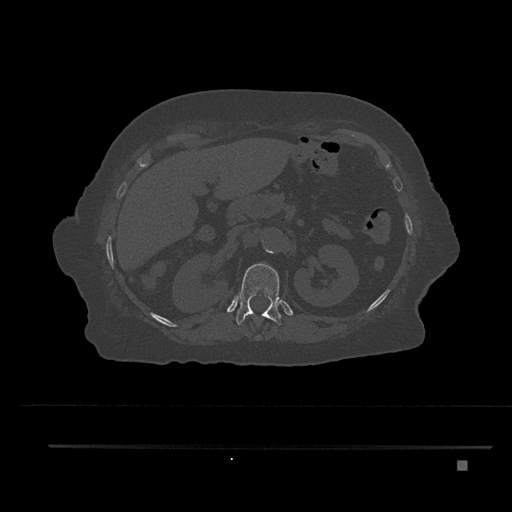
CT including the spine, one axial slice. Position 268 of 797 along the scan axis. Bone window (W 1800 / L 400 HU). 0.5 mm slice thickness. 512 × 512 image matrix, field of view 437 × 437 mm. Female patient, age 76 years. Case-level facts recorded for this patient, not image findings: primary cancer: lung; vertebrae with lytic lesions (as recorded): T11, L3.
Outlined on this slice (semi-automatically segmented with operator editing):
- T11 vertebra: box from (x=244, y=314) to (x=253, y=320) px
- T12 vertebra: (x=236, y=263)–(x=282, y=326)